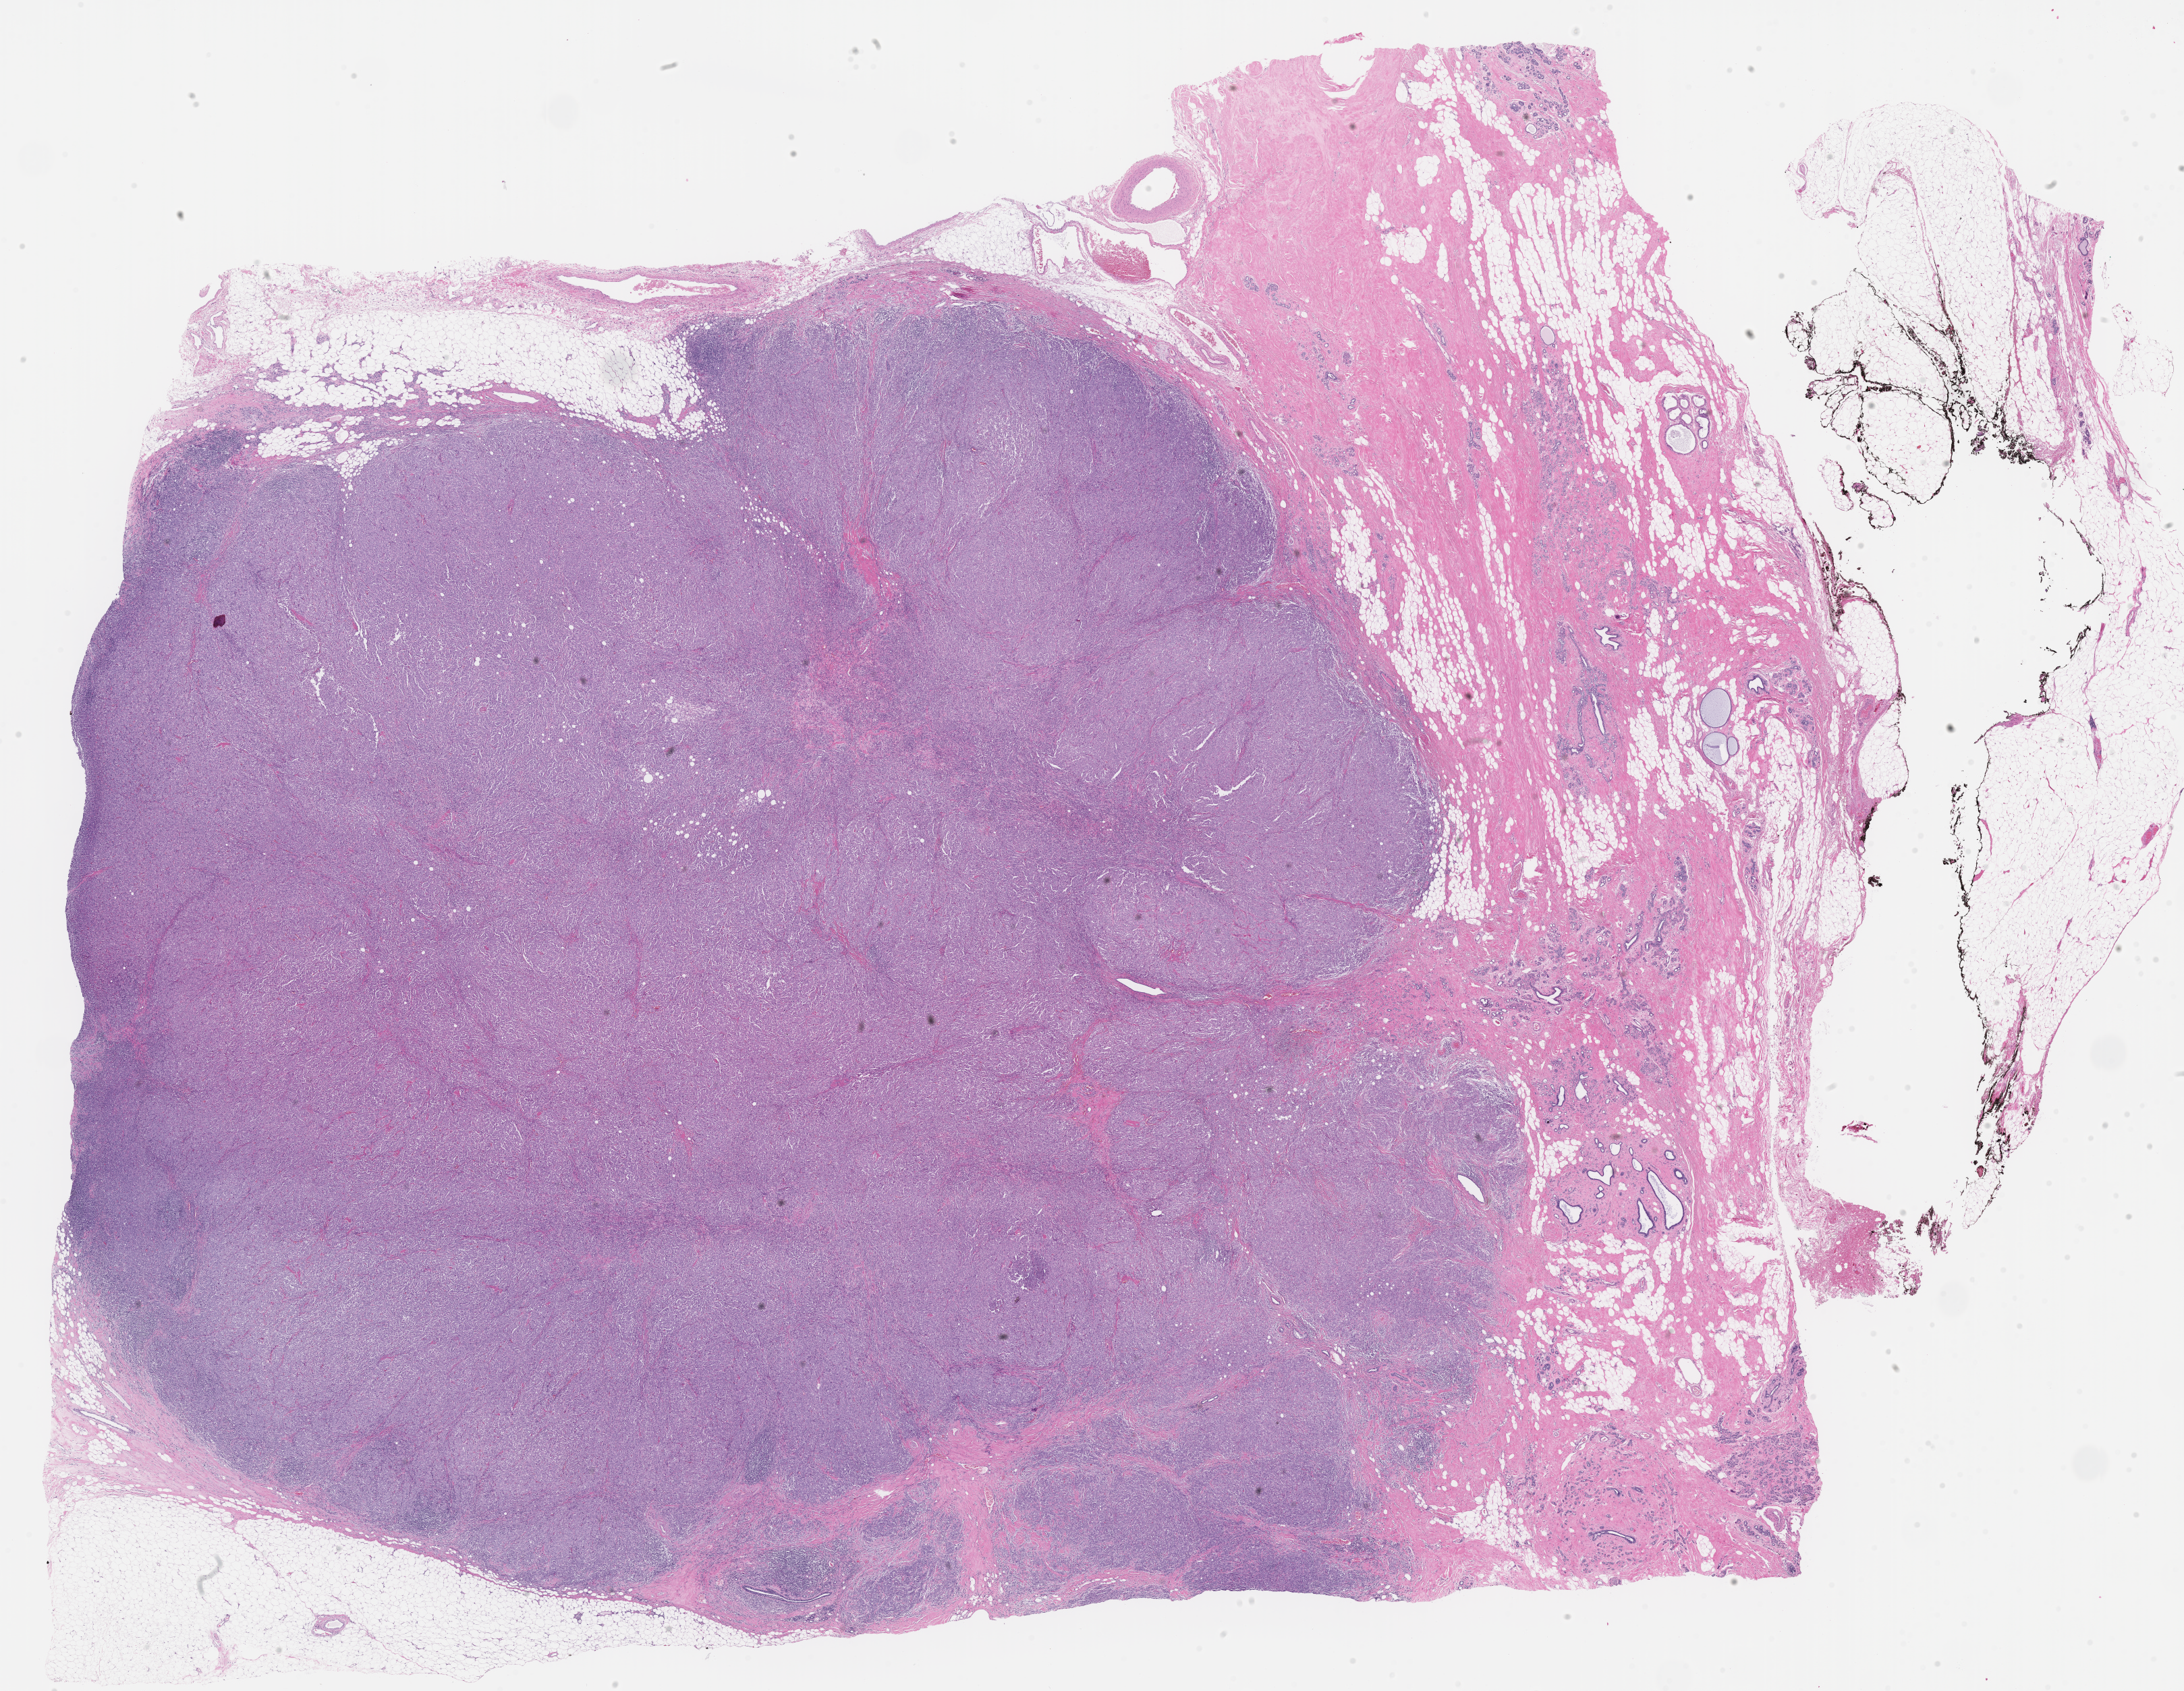
H&E whole-slide image — whole scanned area (about 26.1 x 20.2 mm) shown as a low-resolution overview; formalin-fixed paraffin-embedded section; primary tumor; anatomic site: breast. Female, age 43 years at initial diagnosis. Tumor grade: G3 (poorly differentiated). Pathologist review of this section (percent, as recorded): tumor cells 50%, tumor nuclei 80%, stromal cells 24%, necrosis 0%, normal cells 26%. Infiltration values recorded for this section: lymphocyte infiltration 14%, monocyte infiltration 2%, neutrophil infiltration 0%.
Histologic diagnosis: Lobular carcinoma, NOS. Section: bottom of the tissue portion. AJCC pathologic stage: Stage IIA.